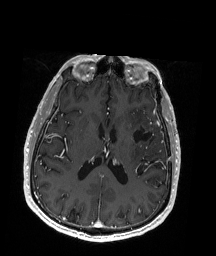
Brain MRI from a brain-tumour surgery series, one axial slice; position 86 of 192 along the scan axis; T1-weighted post-contrast; 216 × 256 image matrix, field of view 211 × 250 mm. From the clinical record (not read from this slice): histopathology: Oligodendroglioma; WHO grade: 2; IDH mutation: yes; tumour location: Left Insular.
Outlined on this slice (outlined manually by an expert reader):
- previous resection cavity: box from (x=132, y=126) to (x=163, y=141) px